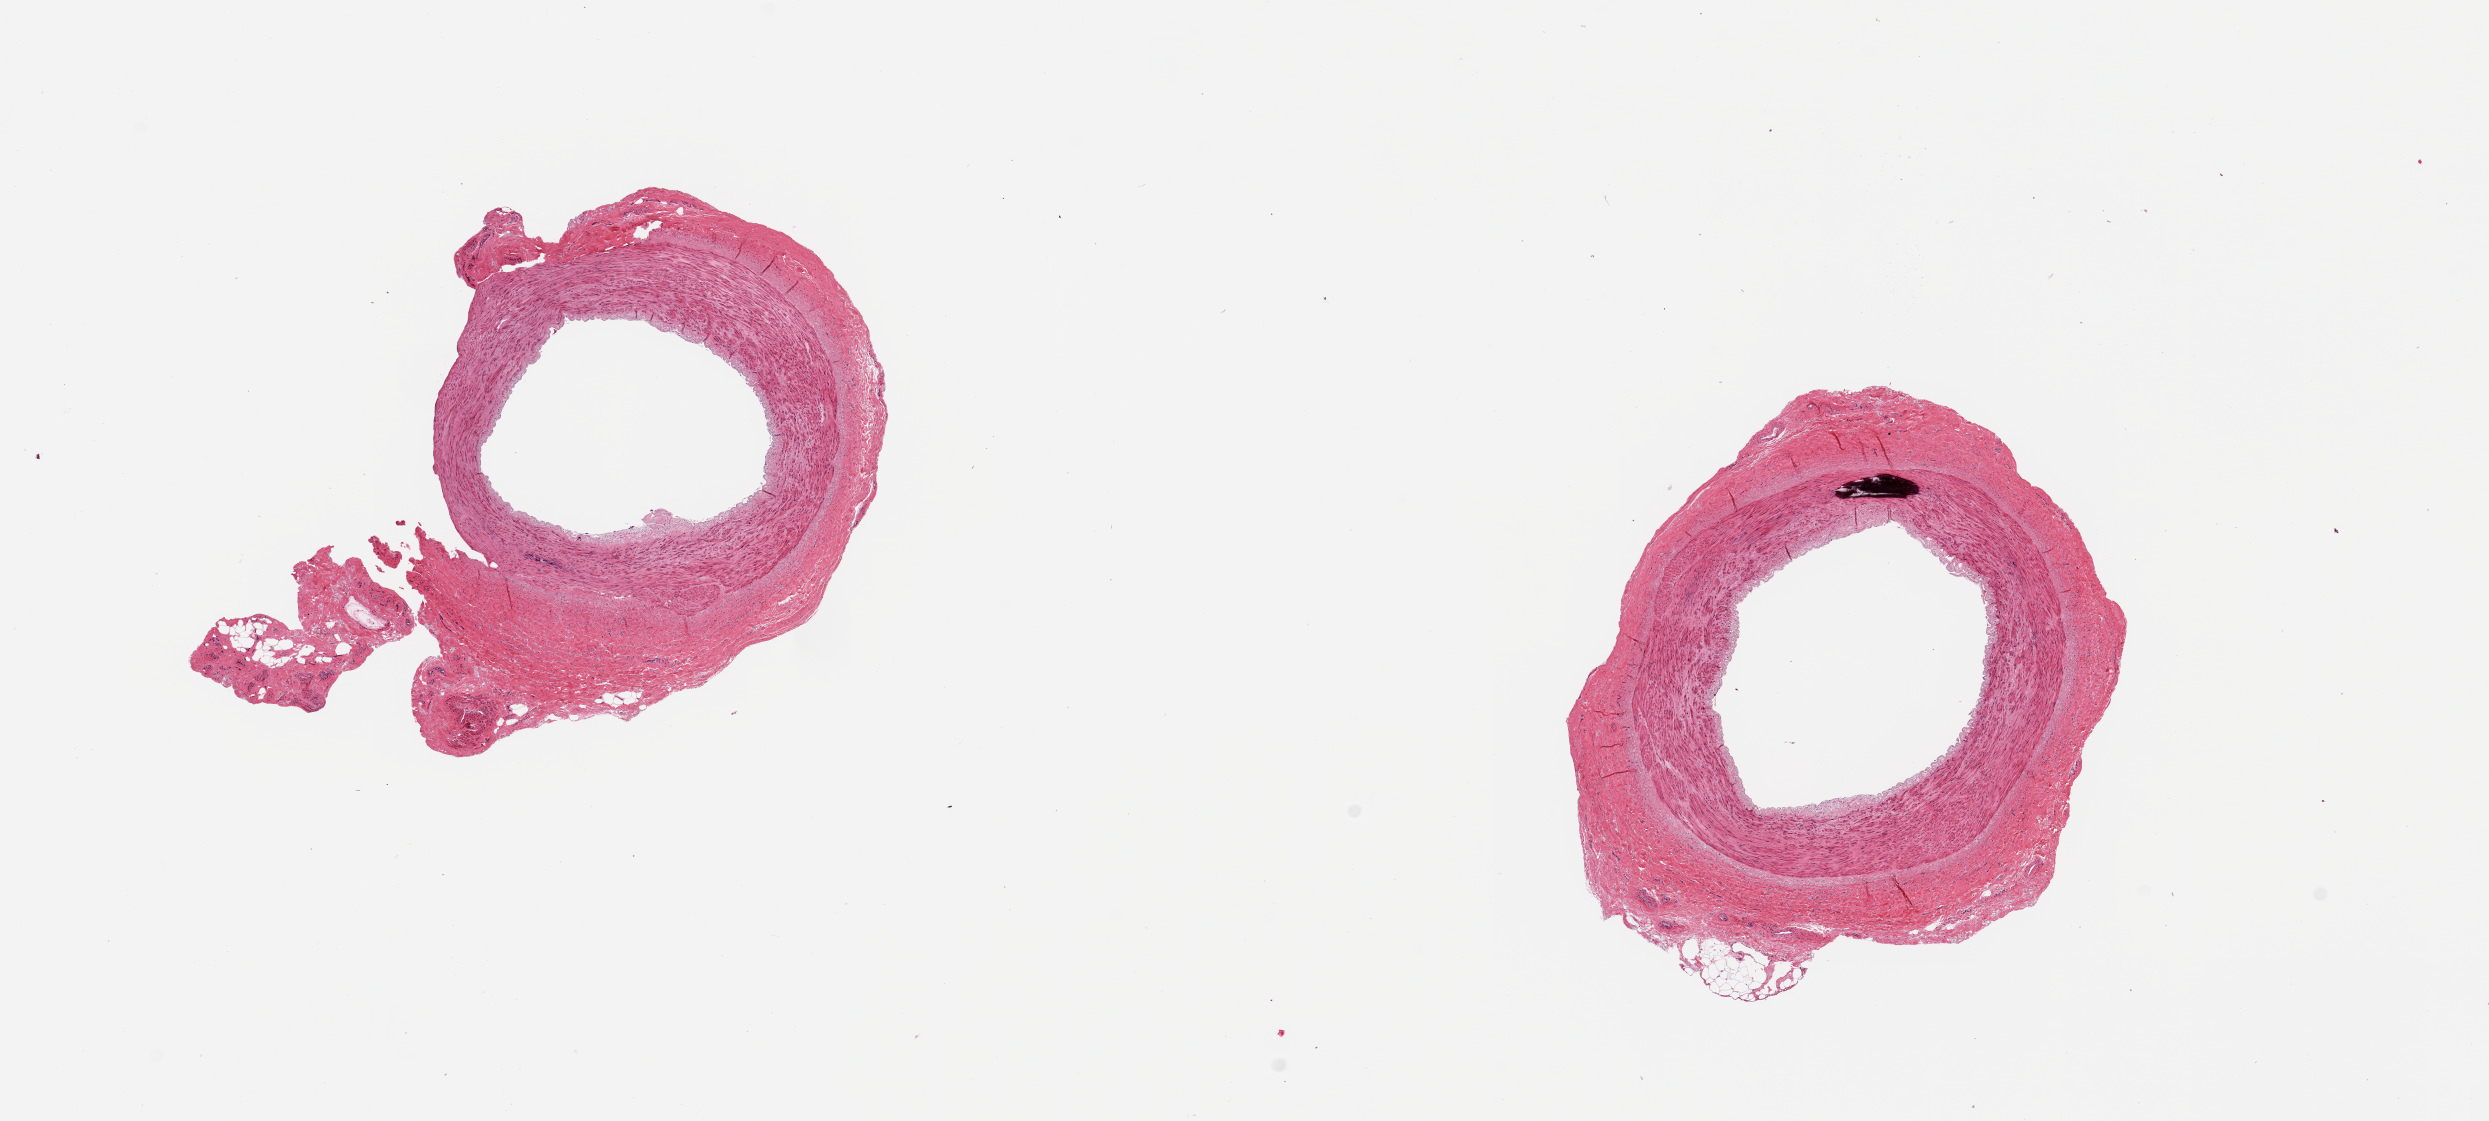
Whole-slide image, hematoxylin and eosin (H&E) stain, whole scanned area (about 19.7 x 8.9 mm) shown as a low-resolution overview, PAXgene-fixed paraffin-embedded (PFPE) section, target tissue: tibial artery, donor tissue sample. Female donor.
- pathologist's review note for this sample: 2 pieces; focal medial calcification